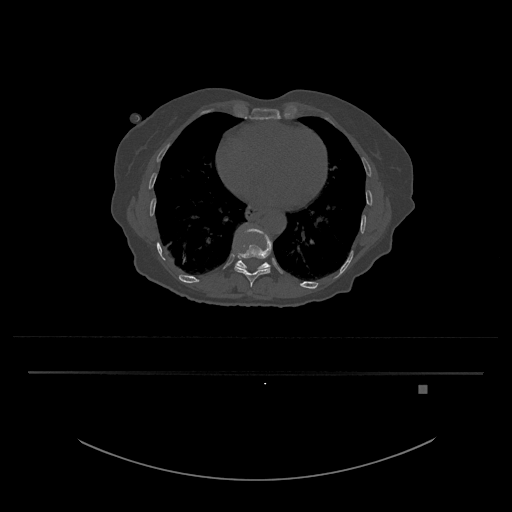
CT including the spine, one axial slice; slice 699 of 797 in the series (ordered by position); reconstruction kernel Br40s/3; 120 kVp; bone window (W 1800 / L 400 HU); 0.5 mm slice thickness; 512 × 512 image matrix. Female patient, age 57 years. Case-level facts recorded for this patient, not image findings: primary cancer: cervical.
Annotated regions visible in this slice (semi-automatically segmented with operator editing):
- T10 vertebra: bounding box (x1, y1, x2, y2) in pixels: (233, 229, 272, 287)
- T11 vertebra: (235, 256, 271, 269)